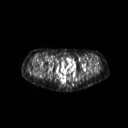
FDG PET of an extremity soft-tissue mass (from a PET/CT study), one axial slice; position 55 of 267 along the scan axis; 3.27 mm slice thickness; 128 × 128 image matrix, field of view 600 × 600 mm. Female patient, age 57 years. Case-level facts recorded for this patient, not image findings: histological type: epithelioid sarcoma with vascular differentiation; site of the primary tumour: right buttock.
Structures marked on this image (expert contour drawn on MRI and transferred to this co-registered scan by the dataset authors):
- gross tumour volume (mass): bounding box <26,67,38,76> (left, top, right, bottom; pixels)